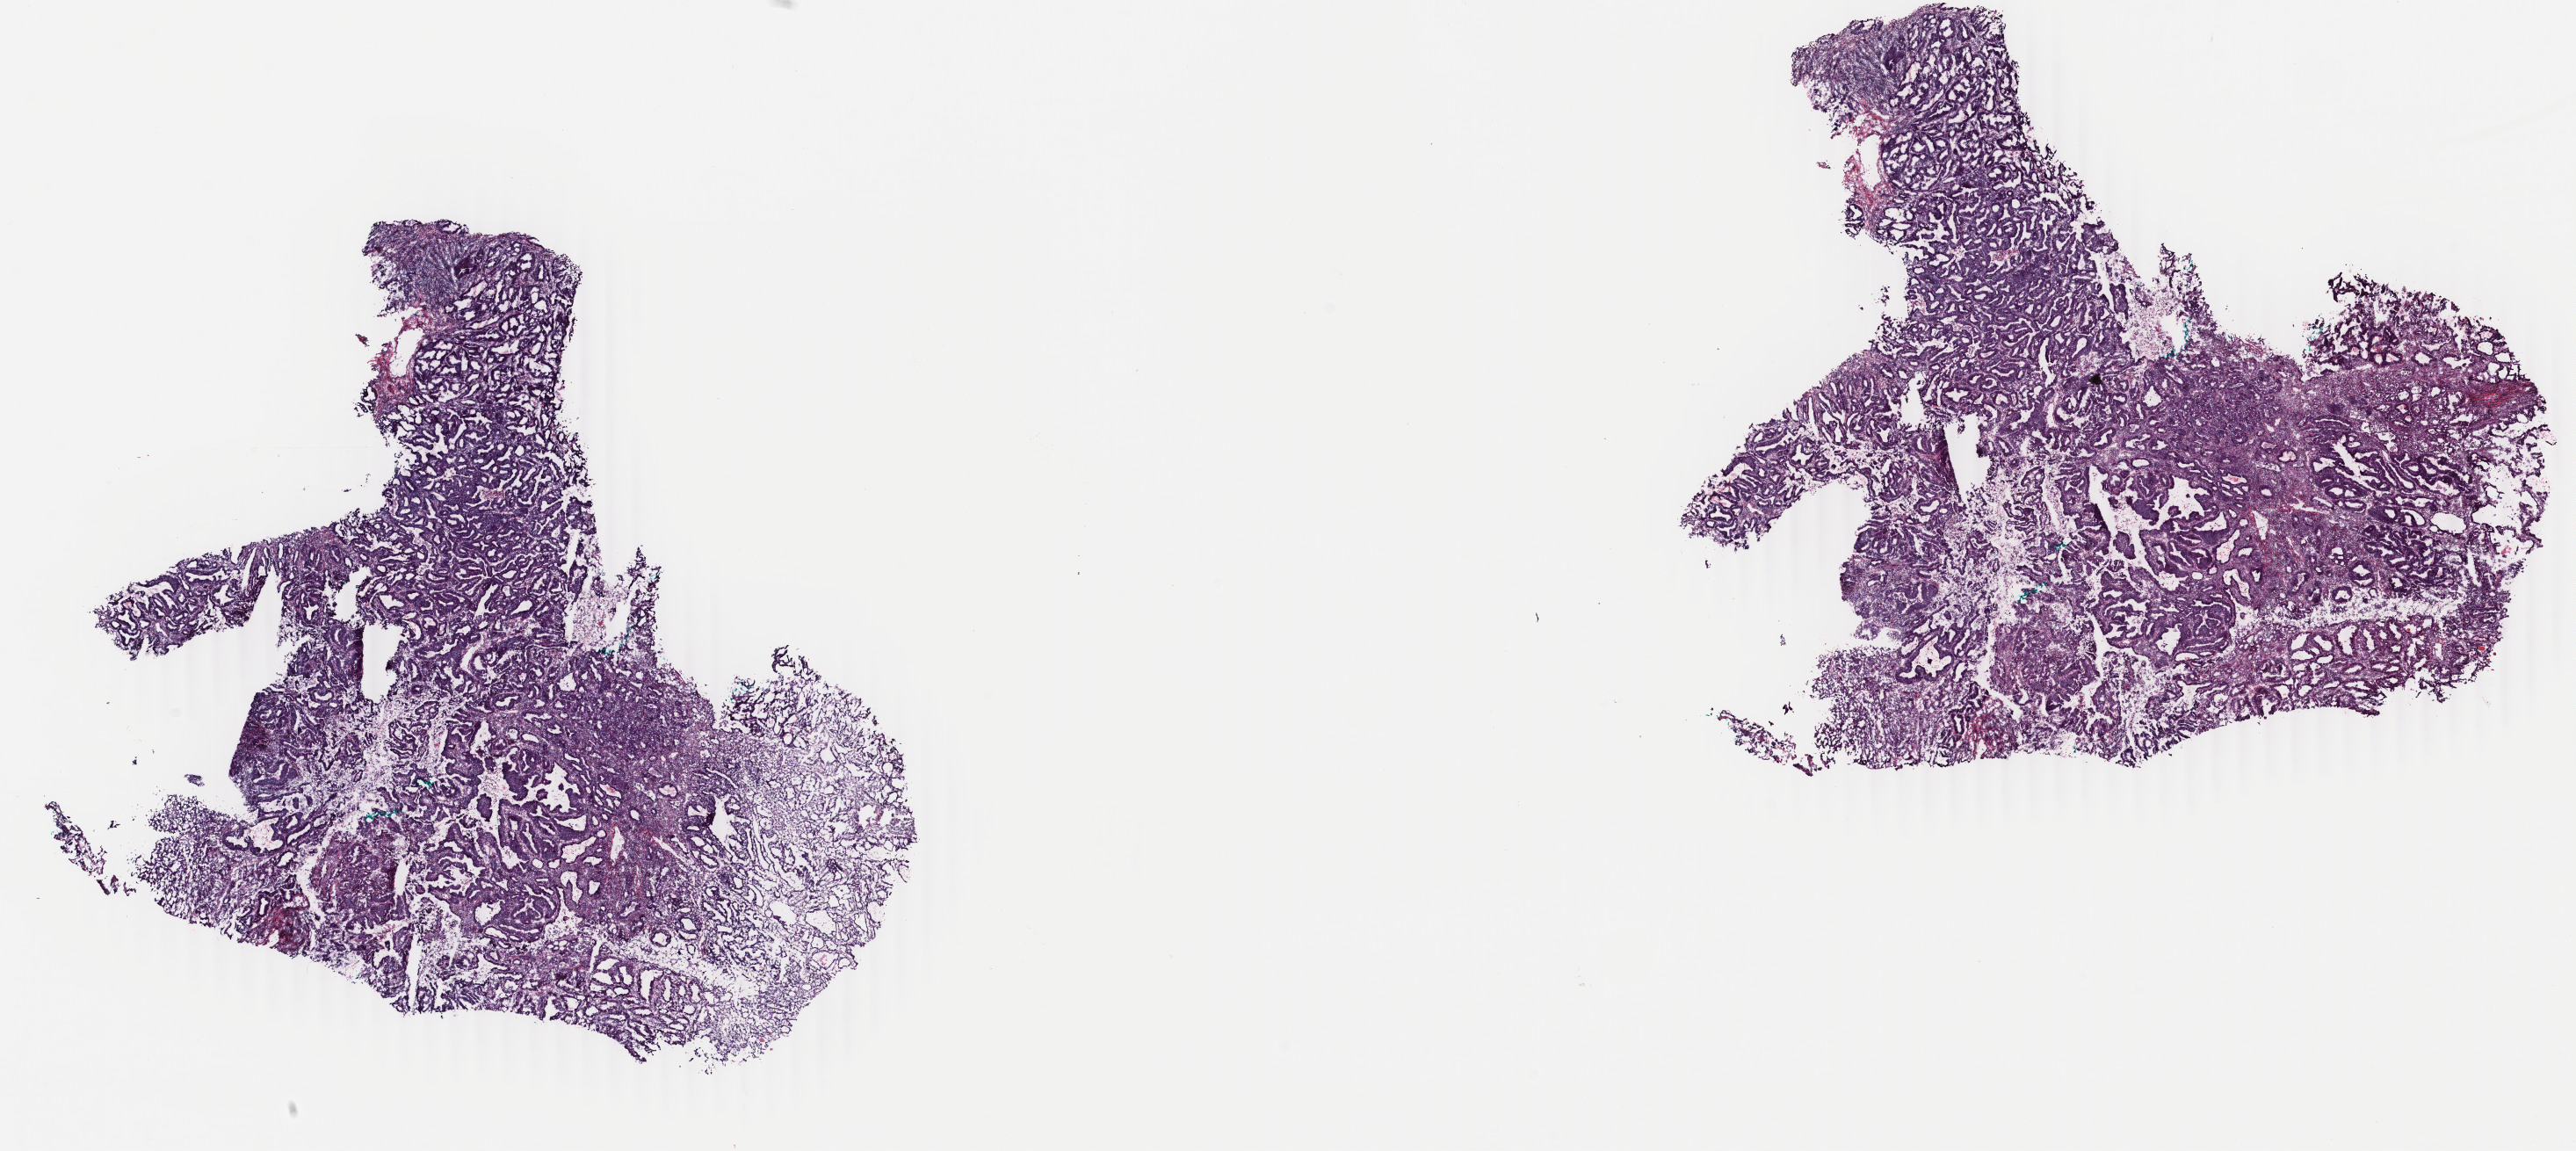
Whole-slide histology image, H&E — a low-resolution overview of the entire scanned area, about 23.3 x 10.4 mm, frozen section, primary tumour sample from the uterus. Female patient; age at initial diagnosis 64 years. Histologic grade: G1 (well differentiated). Slide review estimates, as recorded: tumour cells 100%, tumour nuclei 75%, normal cells 0%, stromal cells 0%, necrosis 0%. Infiltration values recorded for this section: lymphocyte infiltration 0%, monocyte infiltration 0%, neutrophil infiltration 0%.
Histologic diagnosis: Endometrioid adenocarcinoma, NOS (endometrium). FIGO stage: IB. Lymph nodes positive (case pathology): 0 of 5 examined.